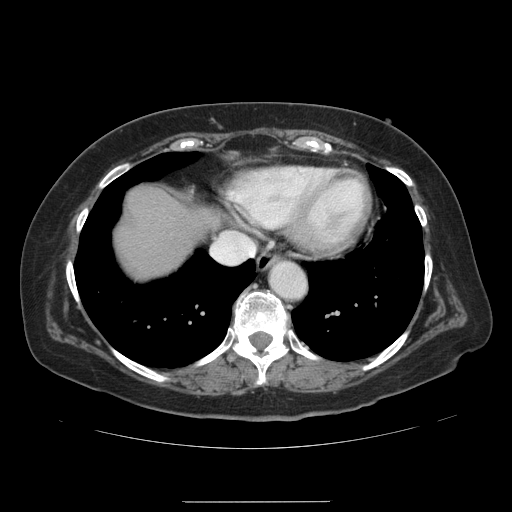
Contrast-enhanced abdominal CT, one axial slice. Position 125 of 141 along the scan axis. Soft-tissue window (W 400 / L 40 HU). 2.5 mm slice thickness. 512 × 512 image matrix, field of view 393 × 393 mm. Female patient, age 74 years. From the clinical record (not read from this slice): diagnosis: colorectal cancer liver metastases, imaged before liver resection; multiple liver metastases: yes; largest metastasis: 7 cm; disease in both lobes: yes.
Annotated regions visible in this slice (expert manual segmentation):
- liver: box from (x=117, y=189) to (x=217, y=279) px
- planned liver remnant (the part of the liver to remain after resection): (x=117, y=189)–(x=217, y=279)